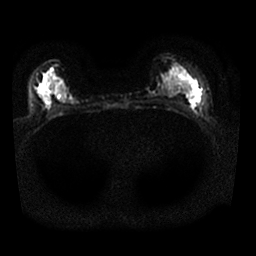
Breast MRI, one axial slice. Position 15 of 25 along the scan axis. Diffusion-weighted series; image 2 of 4 stored at this slice position (different b-values; order by instance number). 1.5 T. 4 mm slice thickness. 256 × 256 image matrix. Female patient.
Annotated regions visible in this slice (outlined manually by an expert reader):
- tumour on diffusion-weighted imaging: bounding box (x1, y1, x2, y2) in pixels: (188, 96, 199, 106)